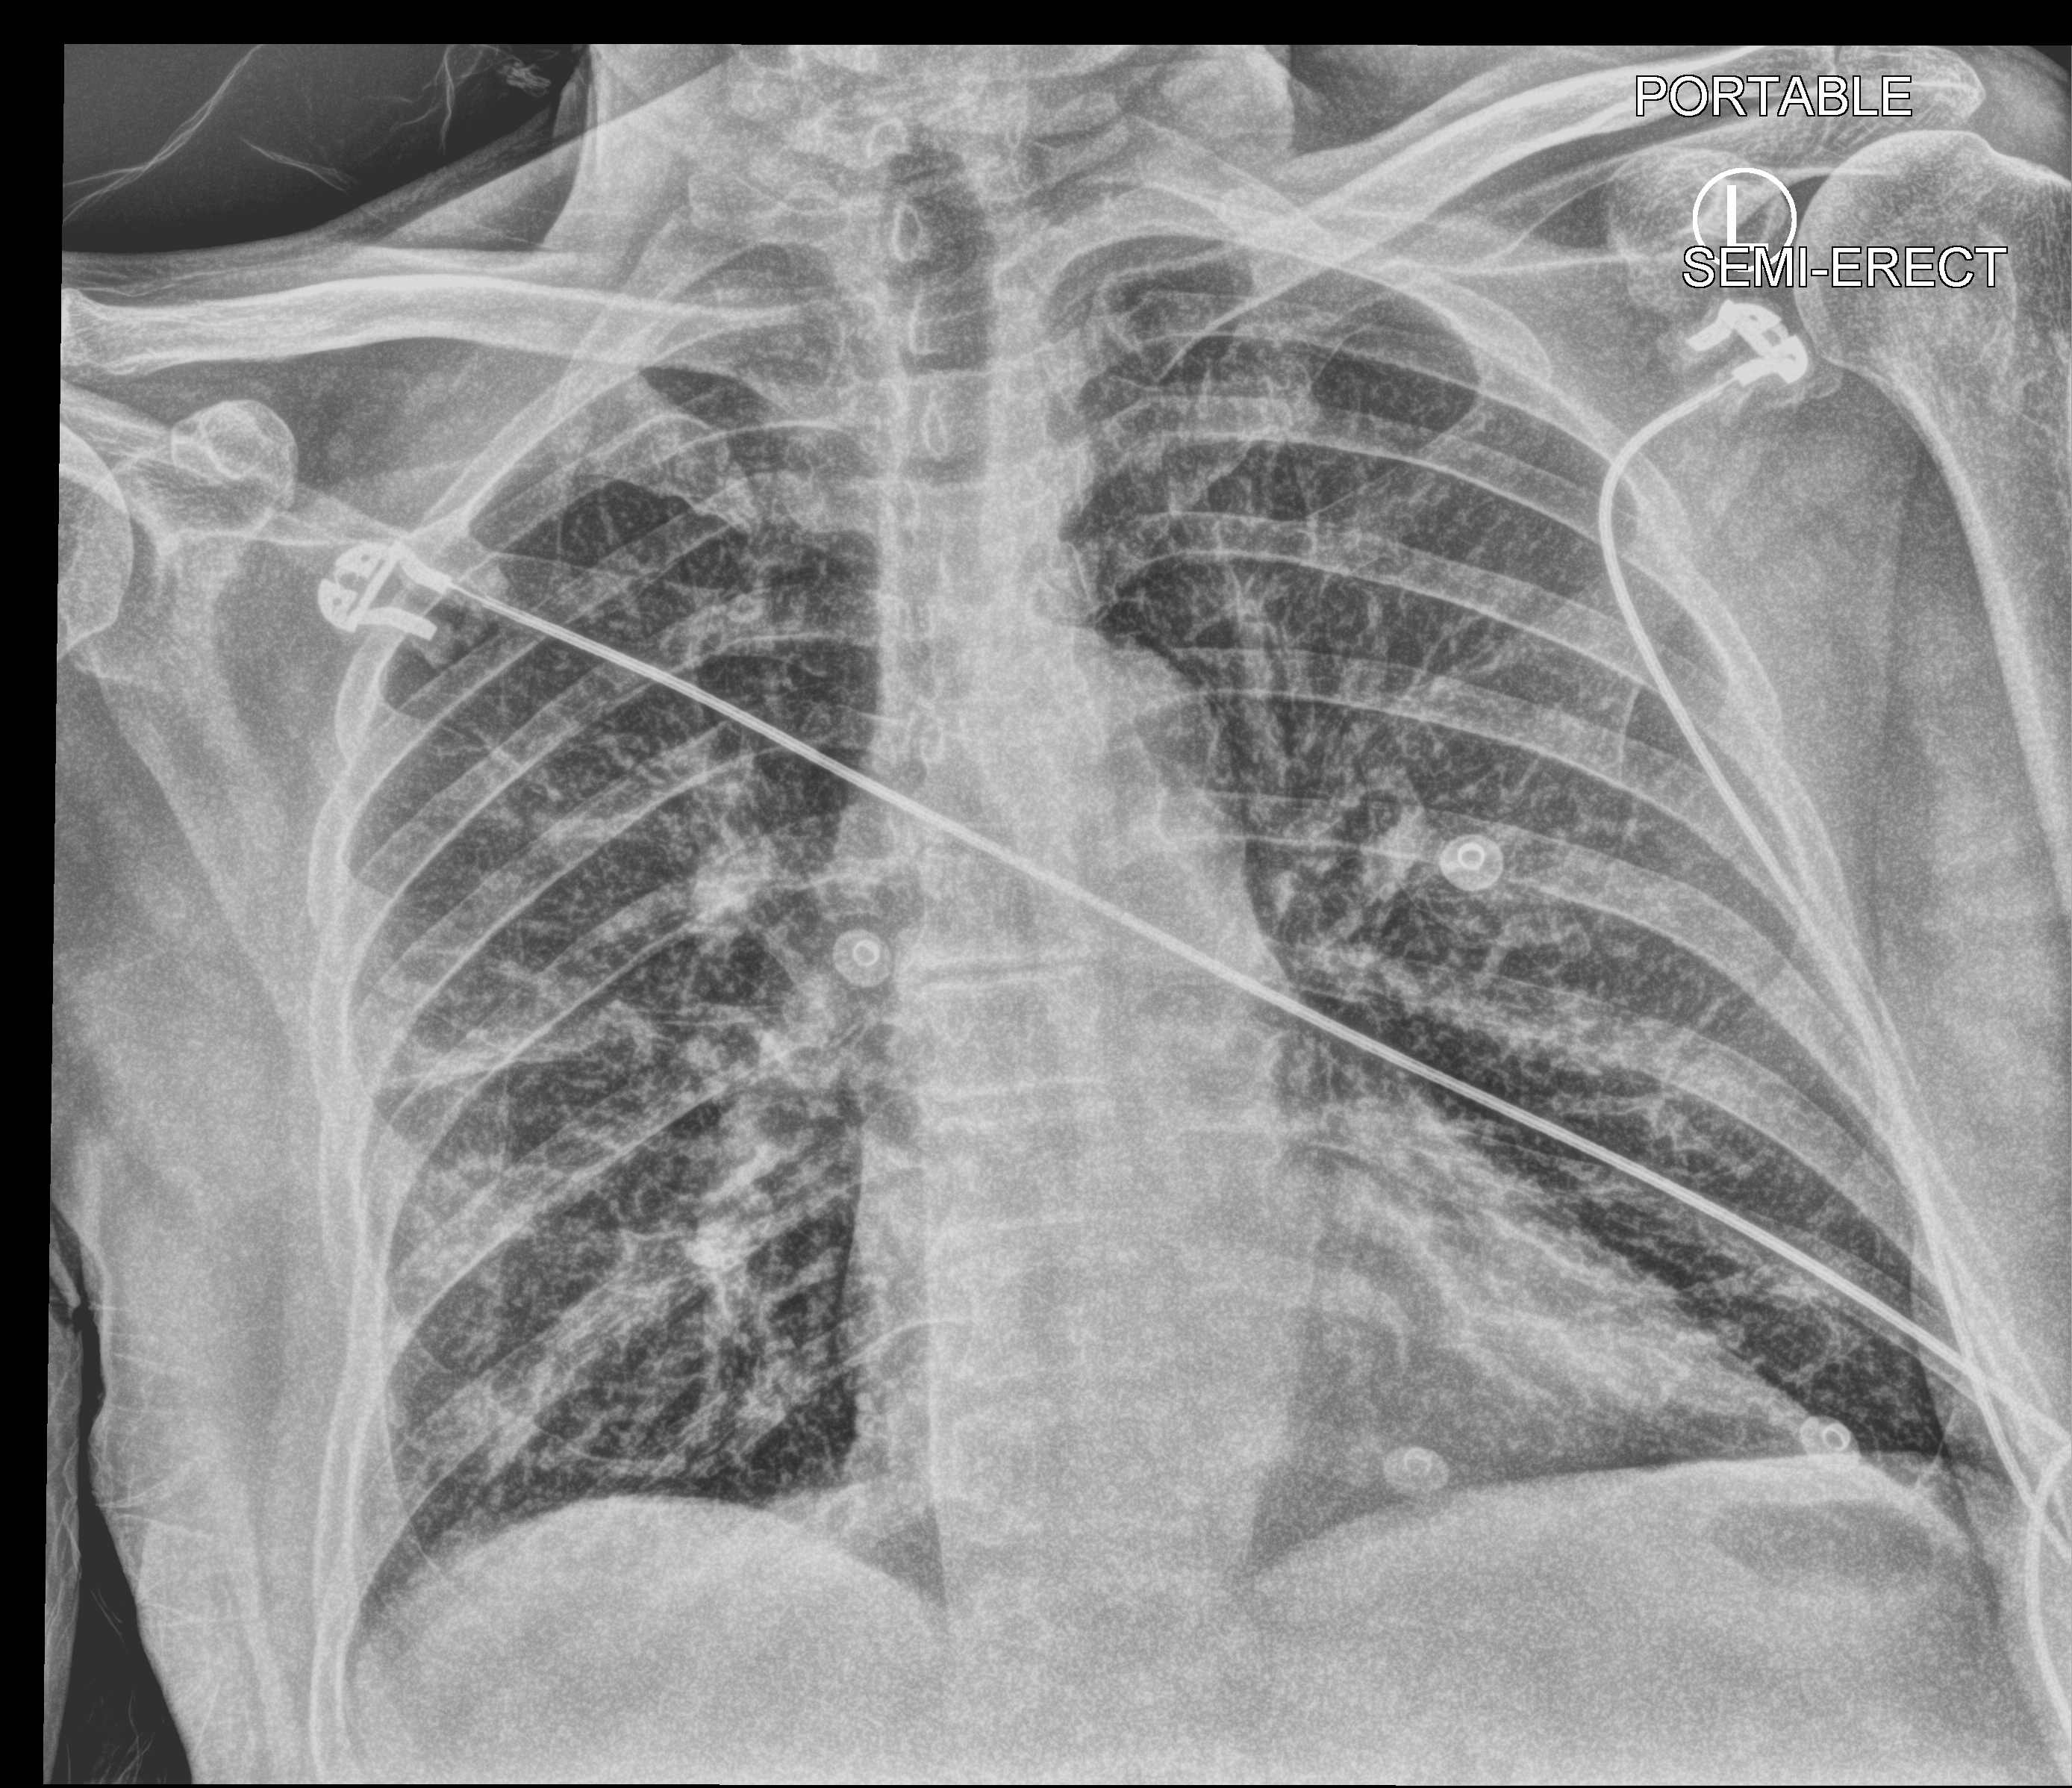
Portable chest radiograph; anteroposterior (AP) projection. Patient hospitalised with COVID-19; male, aged 75–90 years.
Hospital-stay facts (about this admission, not read from this image; timing relative to this image not recorded): admitted to intensive care during this hospital stay: yes; hypertension (admission record): no.